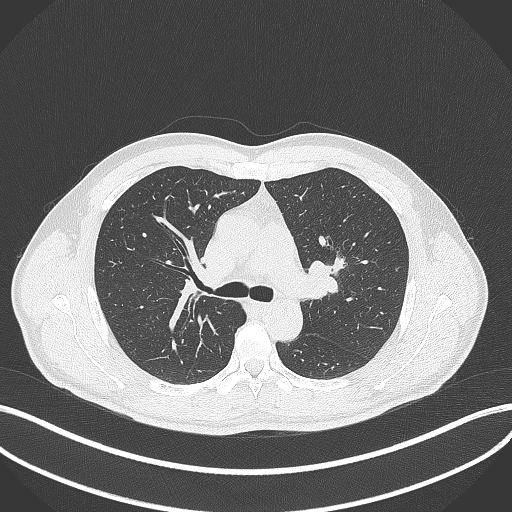
Chest CT, one axial slice; position 274 of 392 along the scan axis; reconstruction kernel B70f; 120 kVp; lung window (W 1500 / L -600 HU); 1 mm slice thickness; 512 × 512 image matrix, field of view 400 × 400 mm. Male patient, age 50 years. From the clinical record (not read from this slice): clinical TNM (as recorded): T1c N1 M1b.
Annotated regions visible in this slice (rectangle marked by the reading radiologist):
- lung tumour (recorded histology: squamous cell carcinoma): box from (x=328, y=252) to (x=346, y=274) px